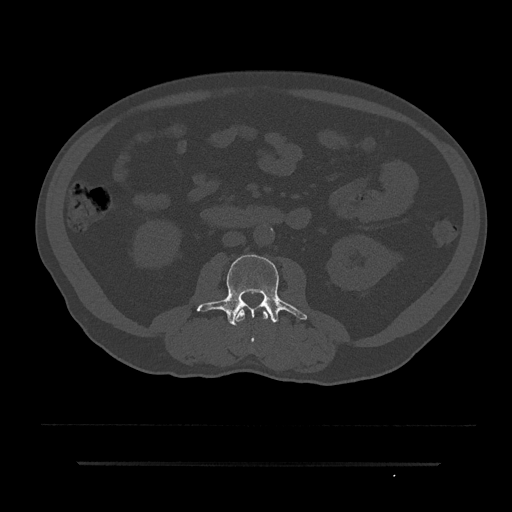
CT including the spine, one axial slice. Position 18 of 797 along the scan axis. Reconstruction kernel Br40s/3. Bone window (W 1800 / L 400 HU). 0.5 mm slice thickness. 512 × 512 image matrix, field of view 464 × 464 mm. Male patient, age 59 years. Case-level facts recorded for this patient, not image findings: primary cancer: bile ducts; vertebrae with lytic lesions (as recorded): T10.
Structures marked on this image (semi-automatic segmentation, software-assisted and operator-edited):
- L2 vertebra: bounding box [x1, y1, x2, y2] px = [234, 307, 269, 323]
- L3 vertebra: [197, 255, 307, 326]